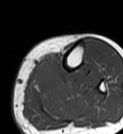
MRI of an extremity soft-tissue mass, one axial slice. Position 17 of 68 along the scan axis. MR volume resampled by the dataset authors to the PET/CT grid (not the native acquisition matrix). 123 × 134 image matrix, field of view 120 × 131 mm. Female patient. Case-level facts recorded for this patient, not image findings: histological type: extraskeletal high grade osteogenic sarcoma; grade: high; site of the primary tumour: left calf.
Structures marked on this image (expert contour drawn on MRI and transferred to this co-registered scan by the dataset authors):
- gross tumour volume (mass): box from (x=33, y=64) to (x=53, y=81) px